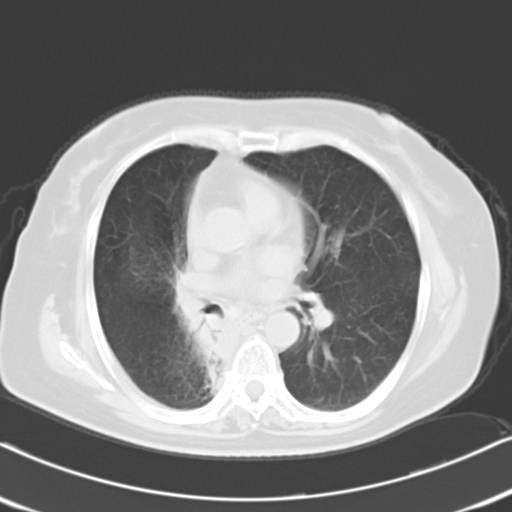
Chest CT, one axial slice; slice 11 of 21 in the series (ordered by position); reconstruction kernel B40f; 120 kVp; lung window (W 1500 / L -600 HU); 10 mm slice thickness; 512 × 512 image matrix. Female patient, age 61 years. From the clinical record (not read from this slice): clinical TNM (as recorded): T1b N0 M1b.
Annotated regions visible in this slice (bounding box drawn by a radiologist):
- lung tumour (recorded histology: squamous cell carcinoma): bounding box [x1, y1, x2, y2] px = [174, 271, 251, 431]